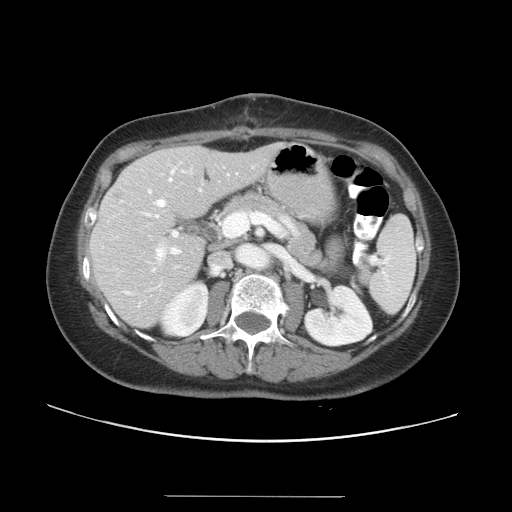
Contrast-enhanced abdominal CT, one axial slice; slice 17 of 34 in the series (ordered by position); intravenous contrast given; soft-tissue window (W 400 / L 40 HU); 5 mm slice thickness; 512 × 512 image matrix, field of view 382 × 382 mm. Female patient, age 69 years. Case-level facts recorded for this patient, not image findings: diagnosis: colorectal cancer liver metastases, imaged before liver resection; multiple liver metastases: yes; largest metastasis: 1.4 cm; chemotherapy before resection: no.
Structures marked on this image (outlined manually by an expert reader):
- hepatic veins: bounding box (x1, y1, x2, y2) in pixels: (152, 169, 180, 271)
- liver: (91, 145, 281, 327)
- planned liver remnant (the part of the liver to remain after resection): (92, 144, 281, 327)
- portal vein (with intrahepatic branches): (156, 212, 377, 262)
- liver metastasis: (109, 185, 127, 203)